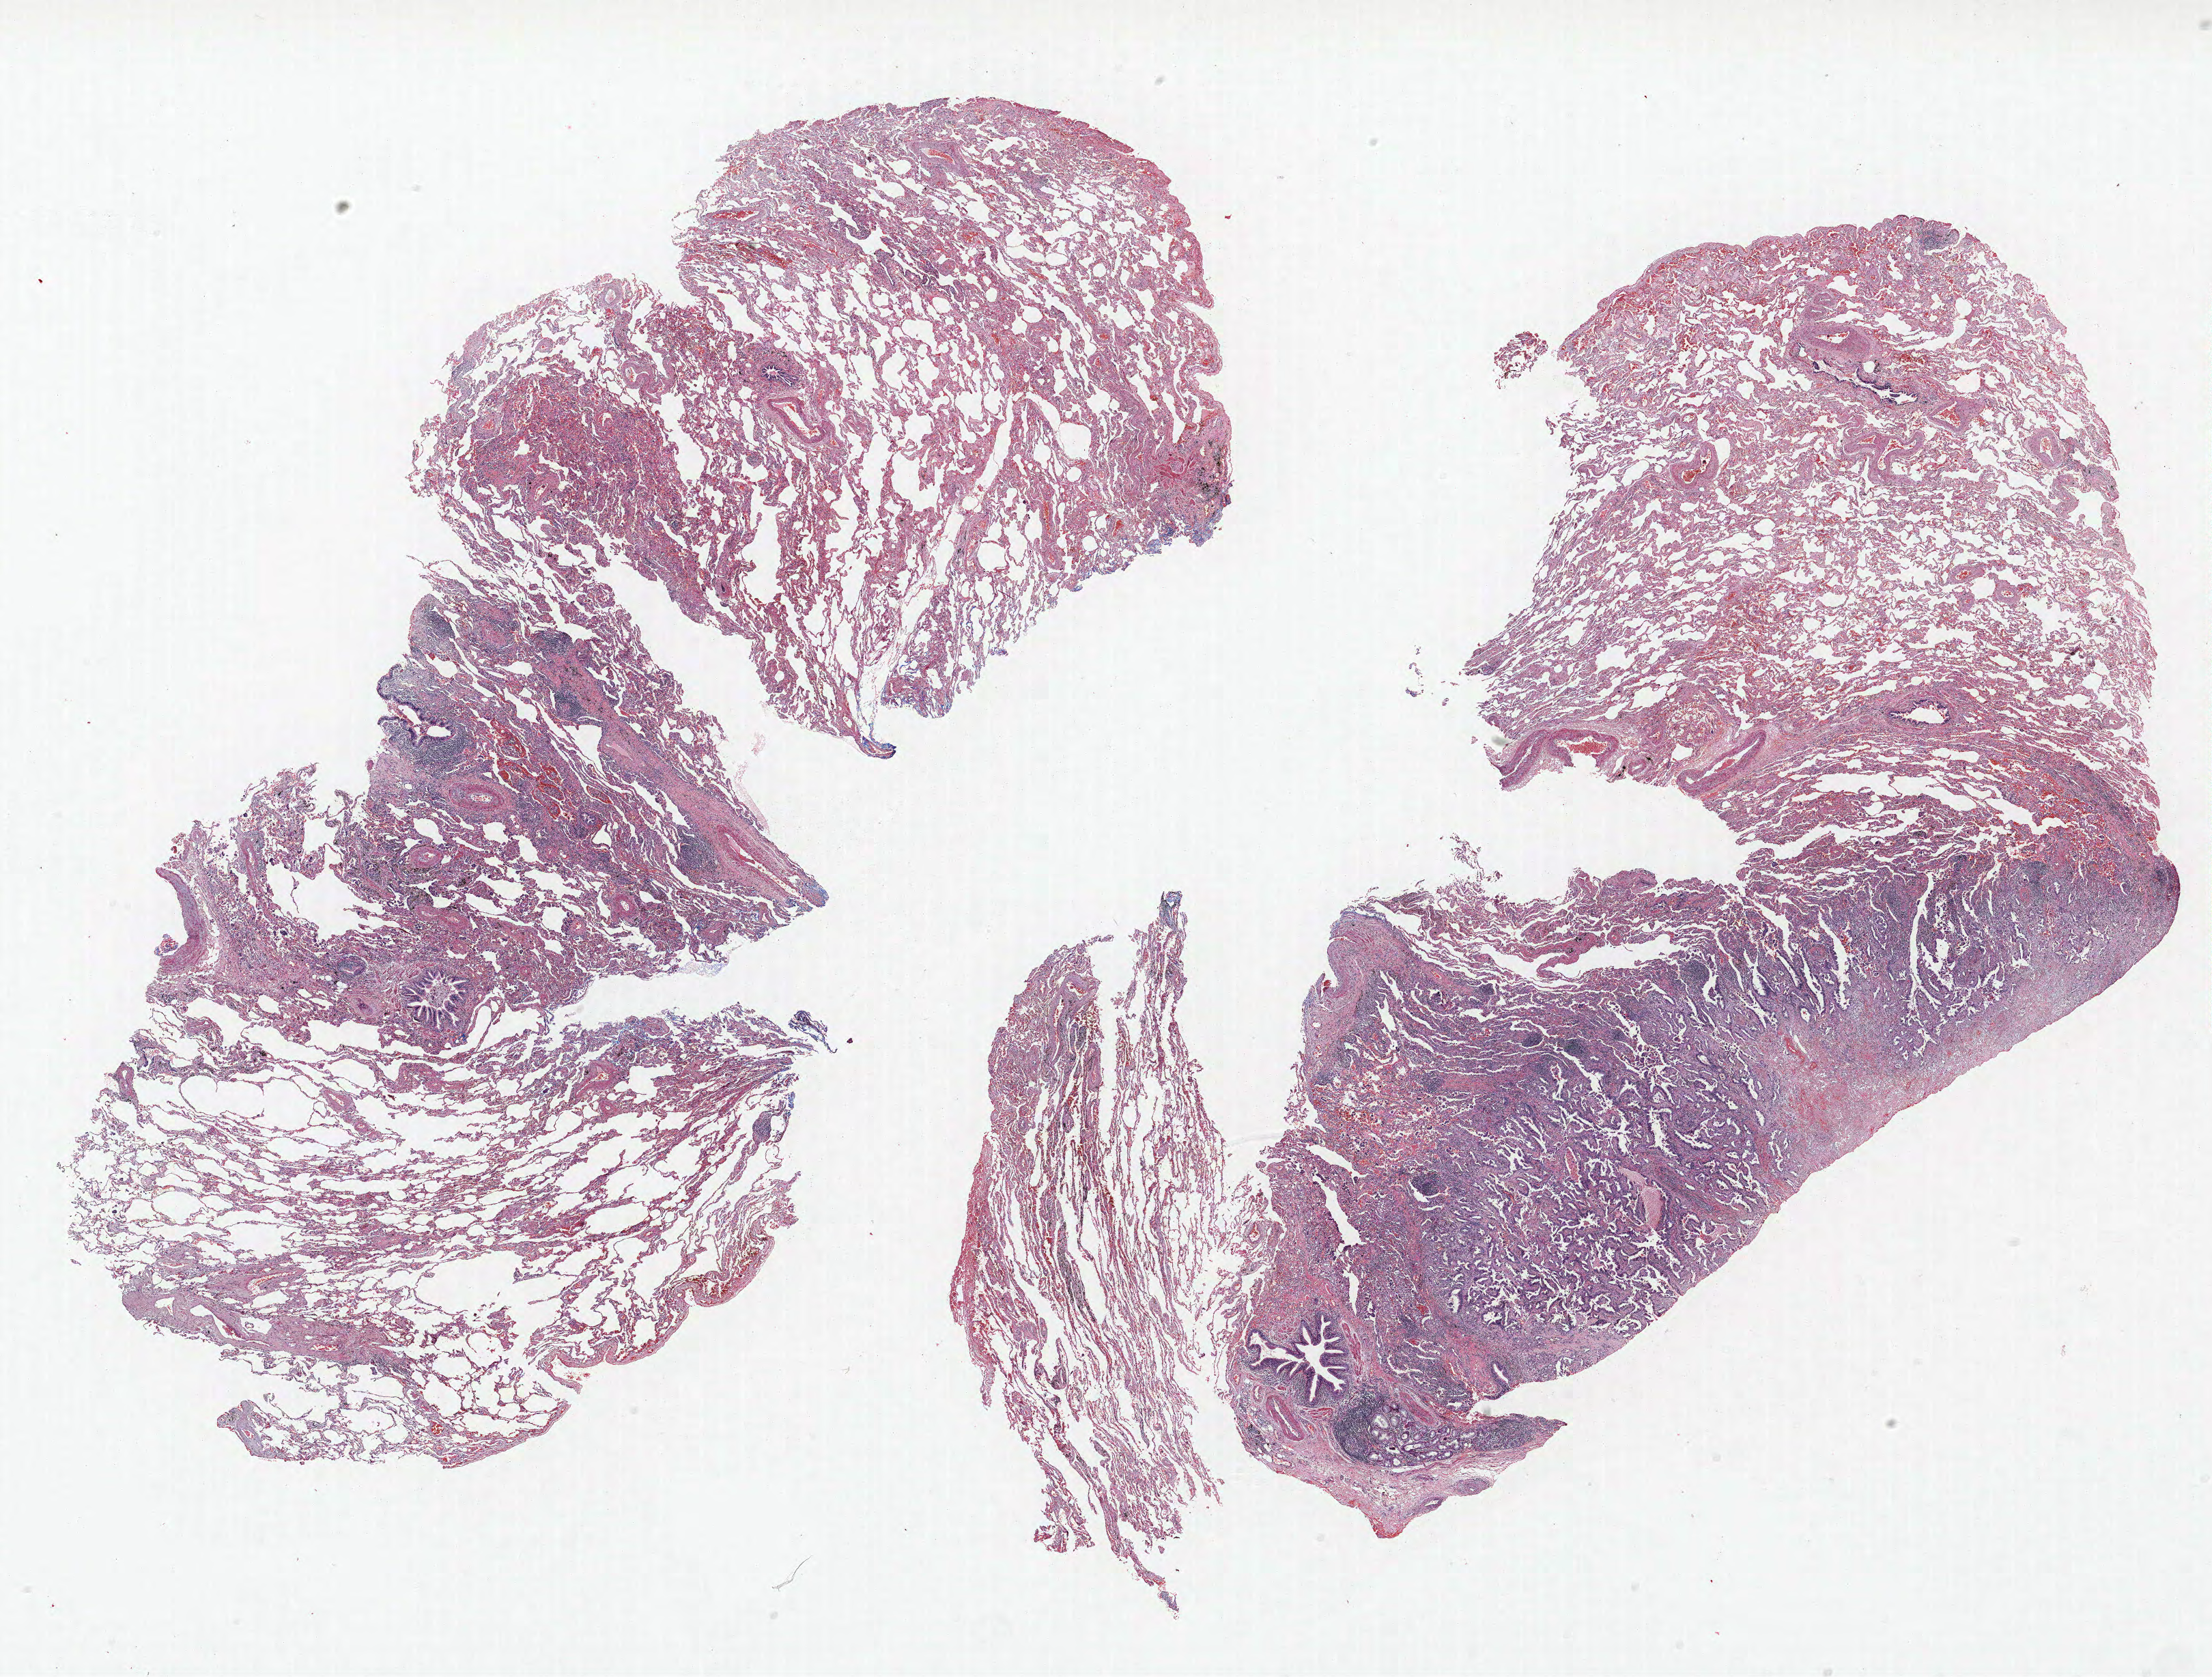
Whole-slide histology image, Hematoxylin and eosin (H&E) stained — shown as a low-resolution overview of the whole scanned area (about 25.9 x 19.7 mm). FFPE section. Lung. Male, age 67 at enrolment. Grade: moderately differentiated (G2).
Primary tumour location (clinical record): right lower lobe. Stage (AJCC 6th edition): IA. Tumour size (pathology): 12 mm. Participant's lung-cancer diagnosis: Adenocarcinoma, NOS (ICD-O-3 8140/3).